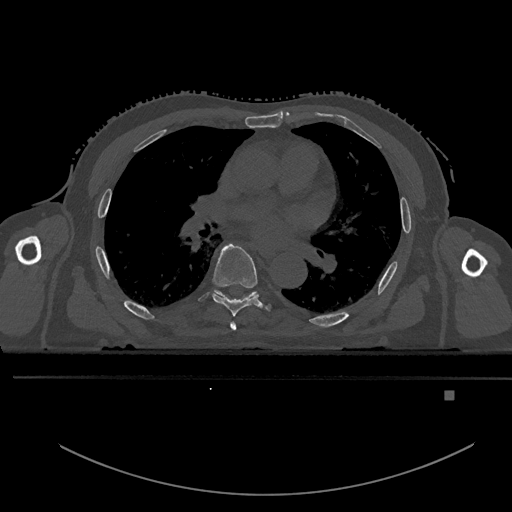
CT including the spine, one axial slice. Slice 301 of 969 in the series (ordered by position). Bone window (W 1800 / L 400 HU). 0.5 mm slice thickness. 512 × 512 image matrix, field of view 456 × 456 mm. Male patient, age 82 years. From the clinical record (not read from this slice): primary cancer: prostate; vertebrae with lytic lesions (as recorded): T11, T9, T8, T2.
Annotated regions visible in this slice (semi-automatic segmentation, software-assisted and operator-edited):
- T5 vertebra: box from (x=230, y=322) to (x=236, y=330) px
- T6 vertebra: (x=212, y=243)–(x=272, y=316)
- T7 vertebra: (x=218, y=292)–(x=256, y=297)